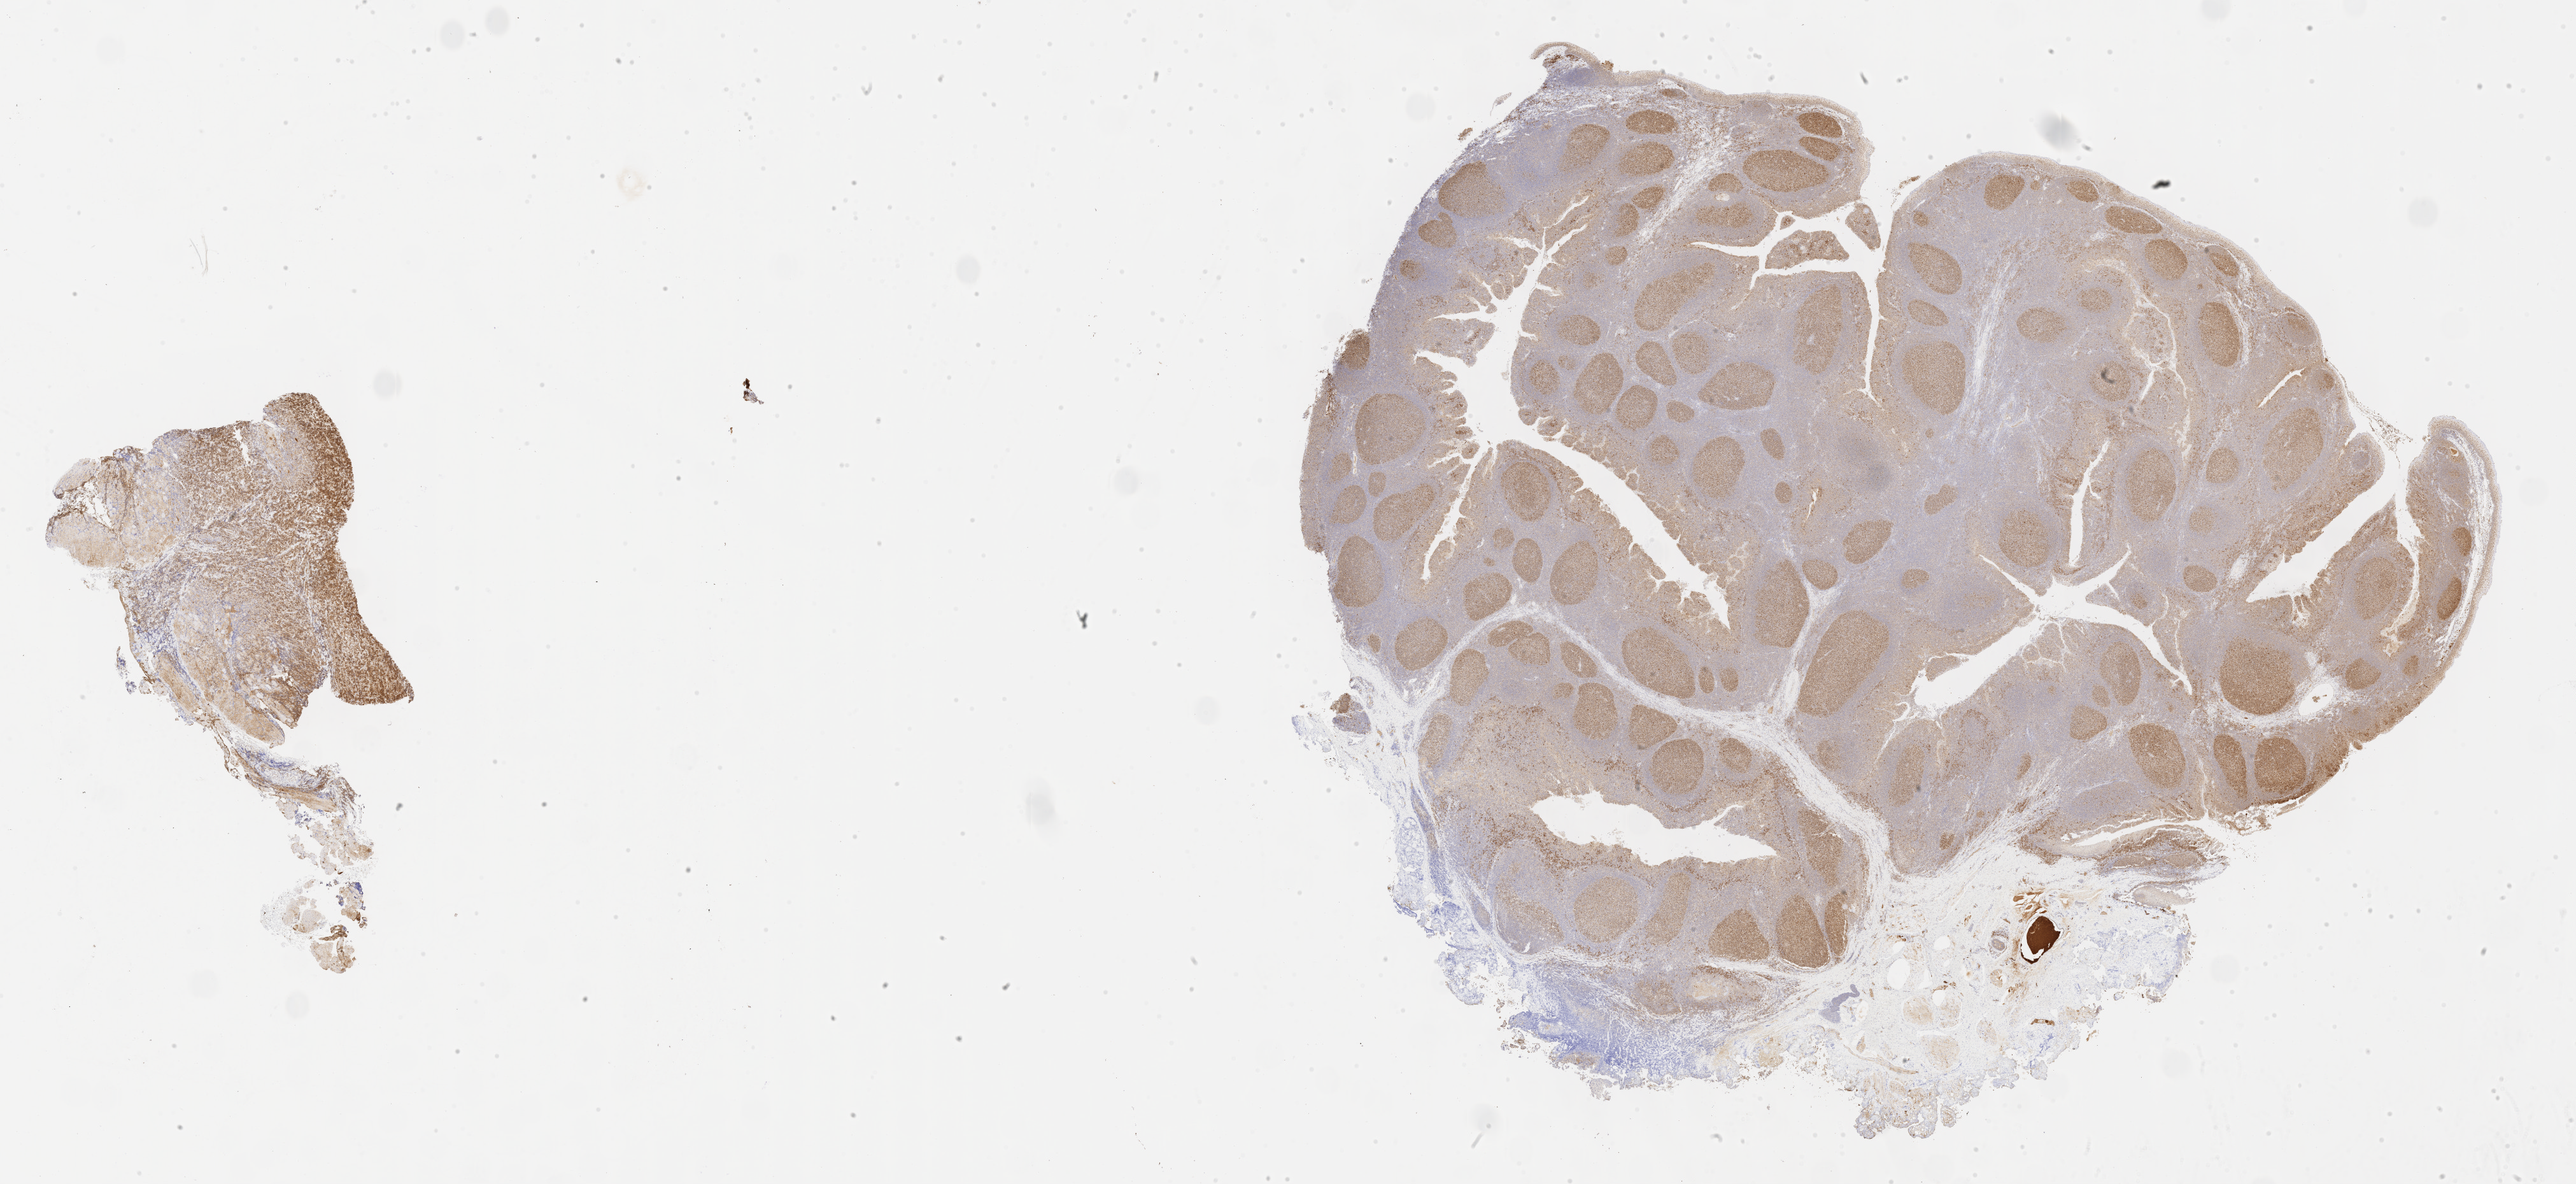
IHC for BCL6, whole-slide image, whole scanned area (about 32.7 x 15.0 mm) shown as a low-resolution overview. Specimen: tumor tissue. Anatomic site: kidney. Male patient, 12 years old.
- histologic diagnosis: Diffuse large B-cell lymphoma, NOS